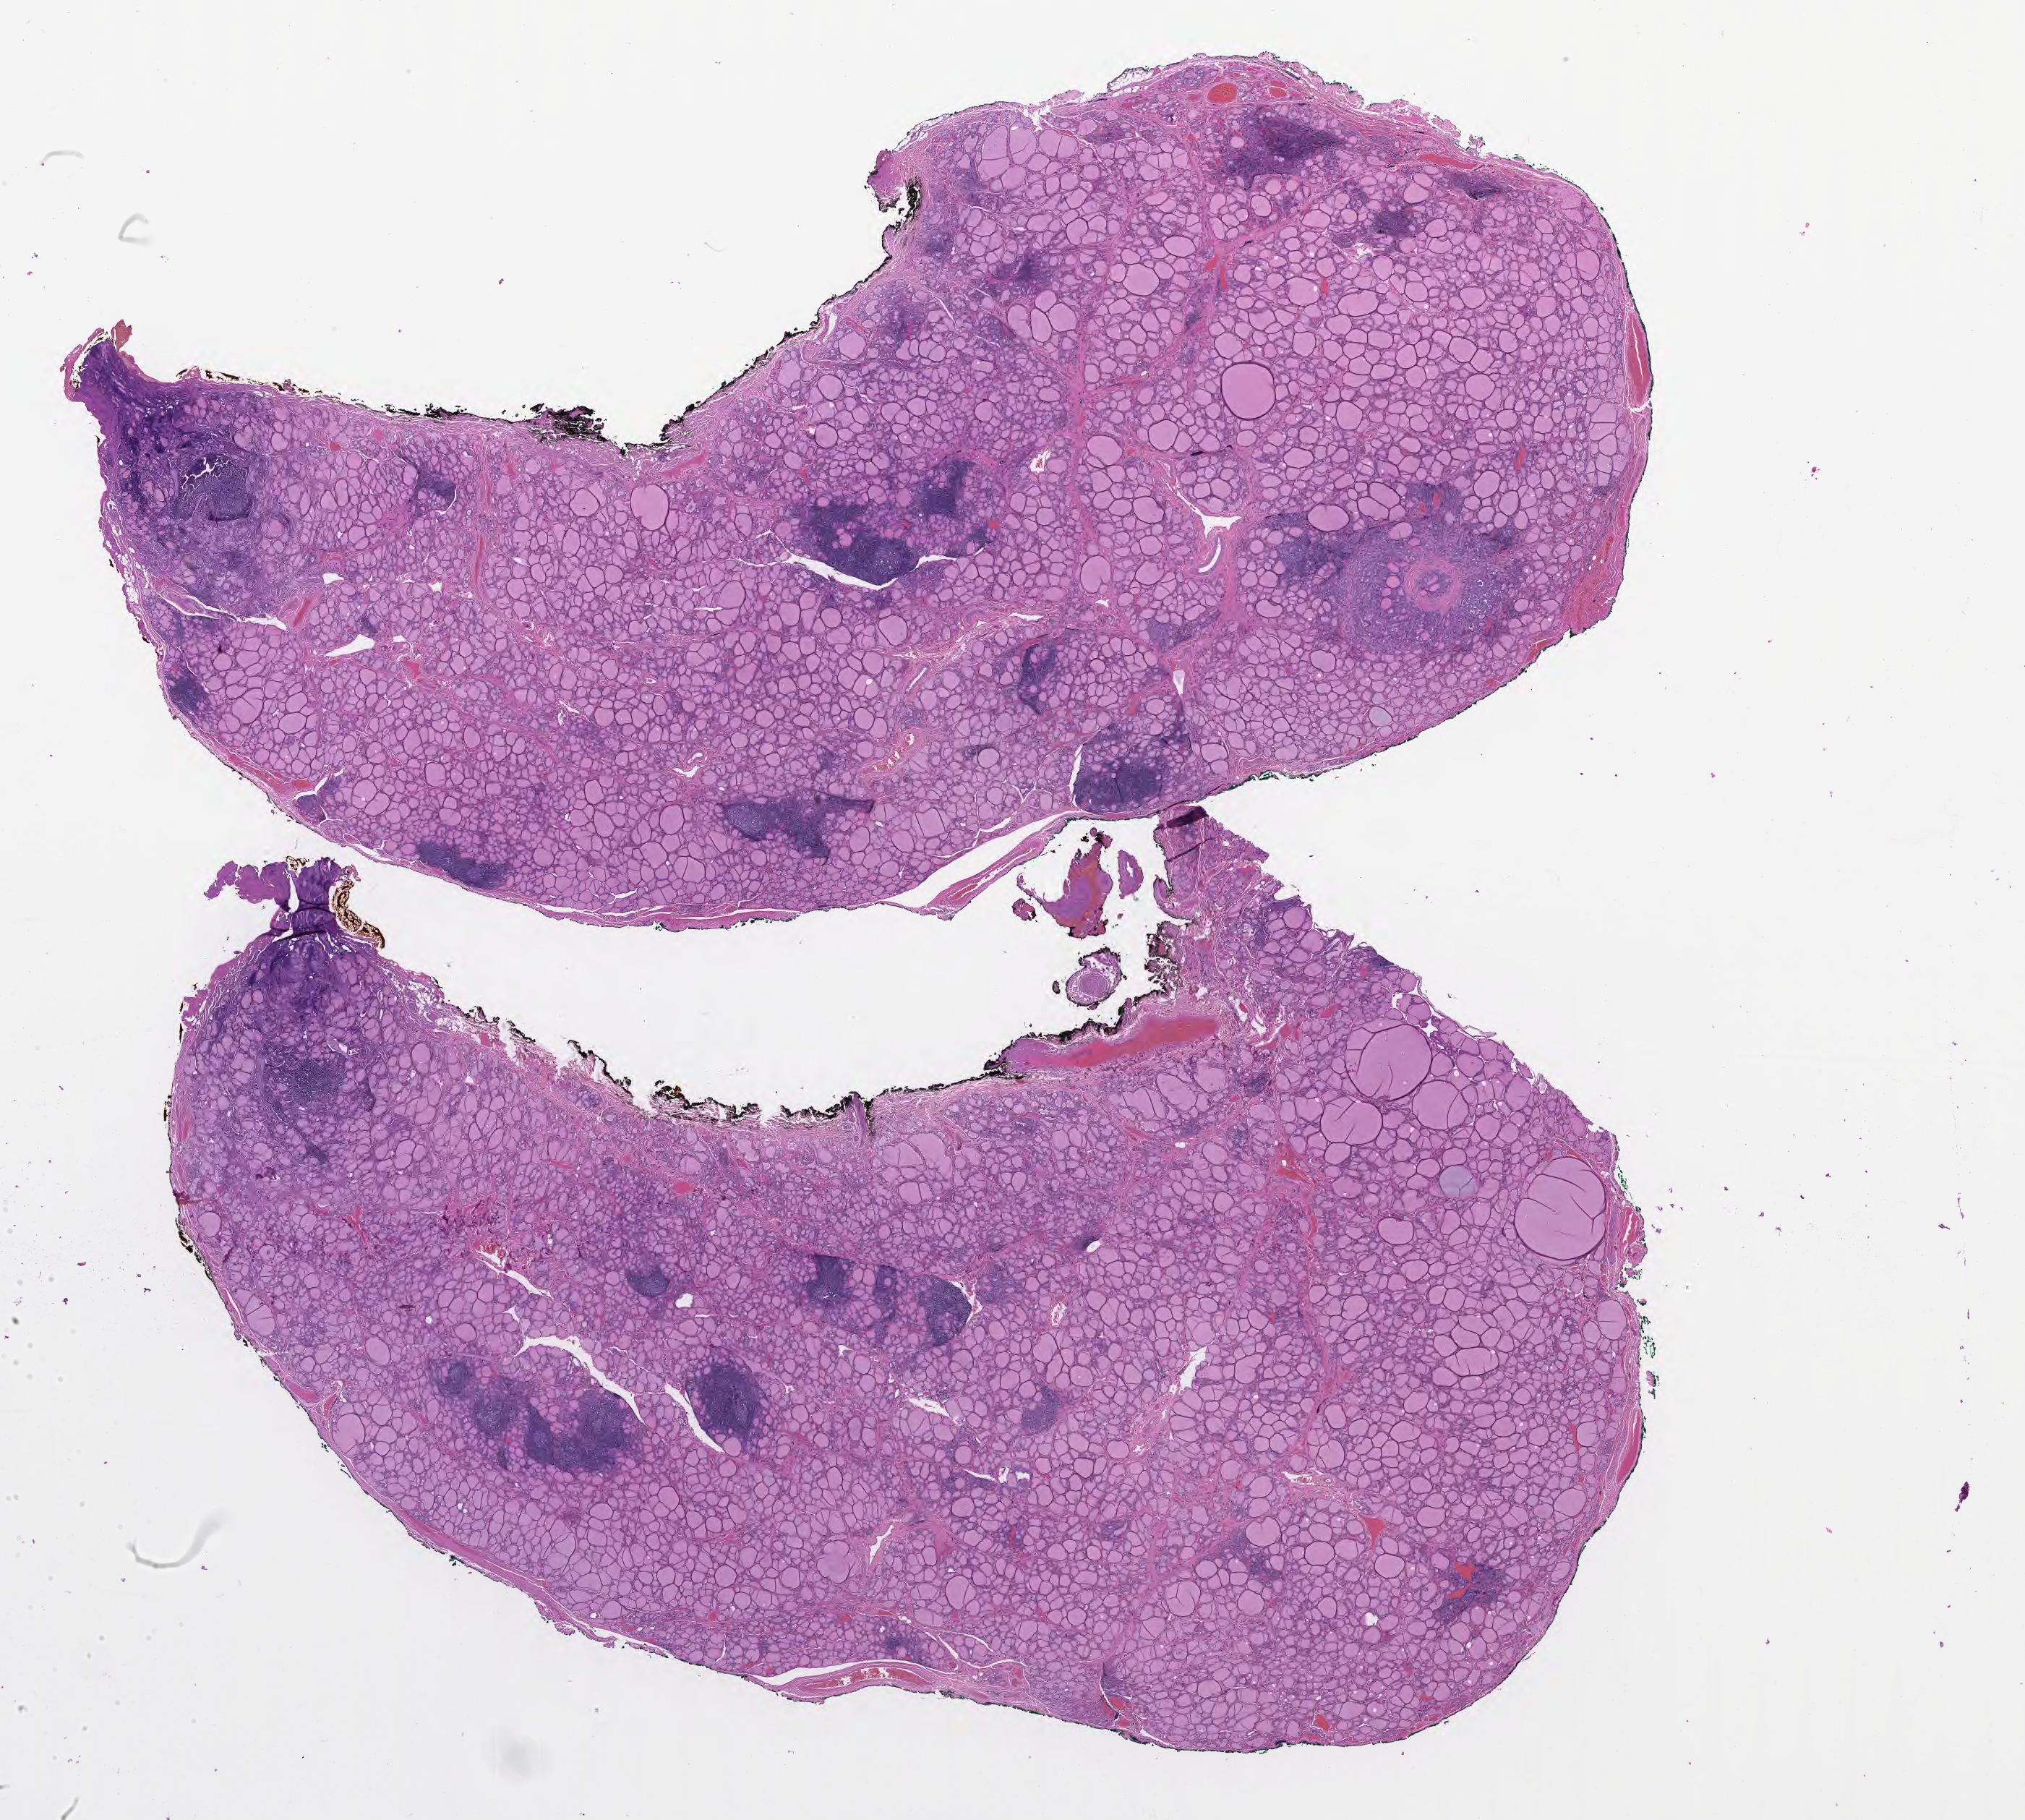
Digitized H&E-stained section of tumor tissue from the thyroid — low-resolution overview of the scanned area, about 22.6 x 20.3 mm; FFPE section. Patient: male, age 208 months (17 years 4 months).
- diagnosis (ICD-O-3 morphology term): Papillary microcarcinoma